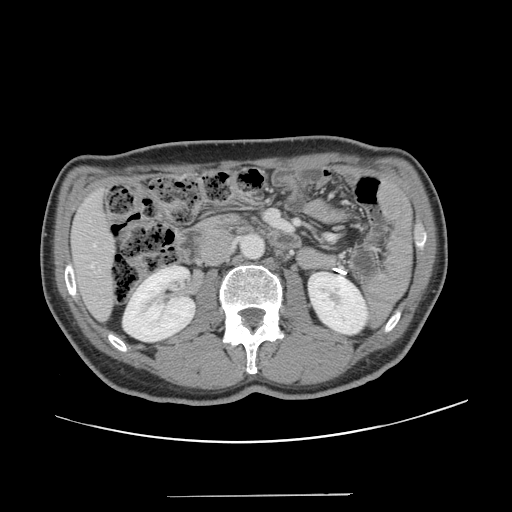
Contrast-enhanced abdominal CT, one axial slice; 120 kVp; intravenous contrast given; soft-tissue window (W 400 / L 40 HU); 2.5 mm slice thickness; 512 × 512 image matrix, field of view 403 × 403 mm. Male patient, age 60 years. From the clinical record (not read from this slice): diagnosis: colorectal cancer liver metastases, imaged before liver resection; multiple liver metastases: no; largest metastasis: 2.5 cm; disease in both lobes: no.
Outlined on this slice (manually delineated by an expert):
- hepatic veins: box from (x=91, y=245) to (x=96, y=267) px
- liver: (x=72, y=195)–(x=113, y=318)
- planned liver remnant (the part of the liver to remain after resection): (x=72, y=194)–(x=113, y=318)